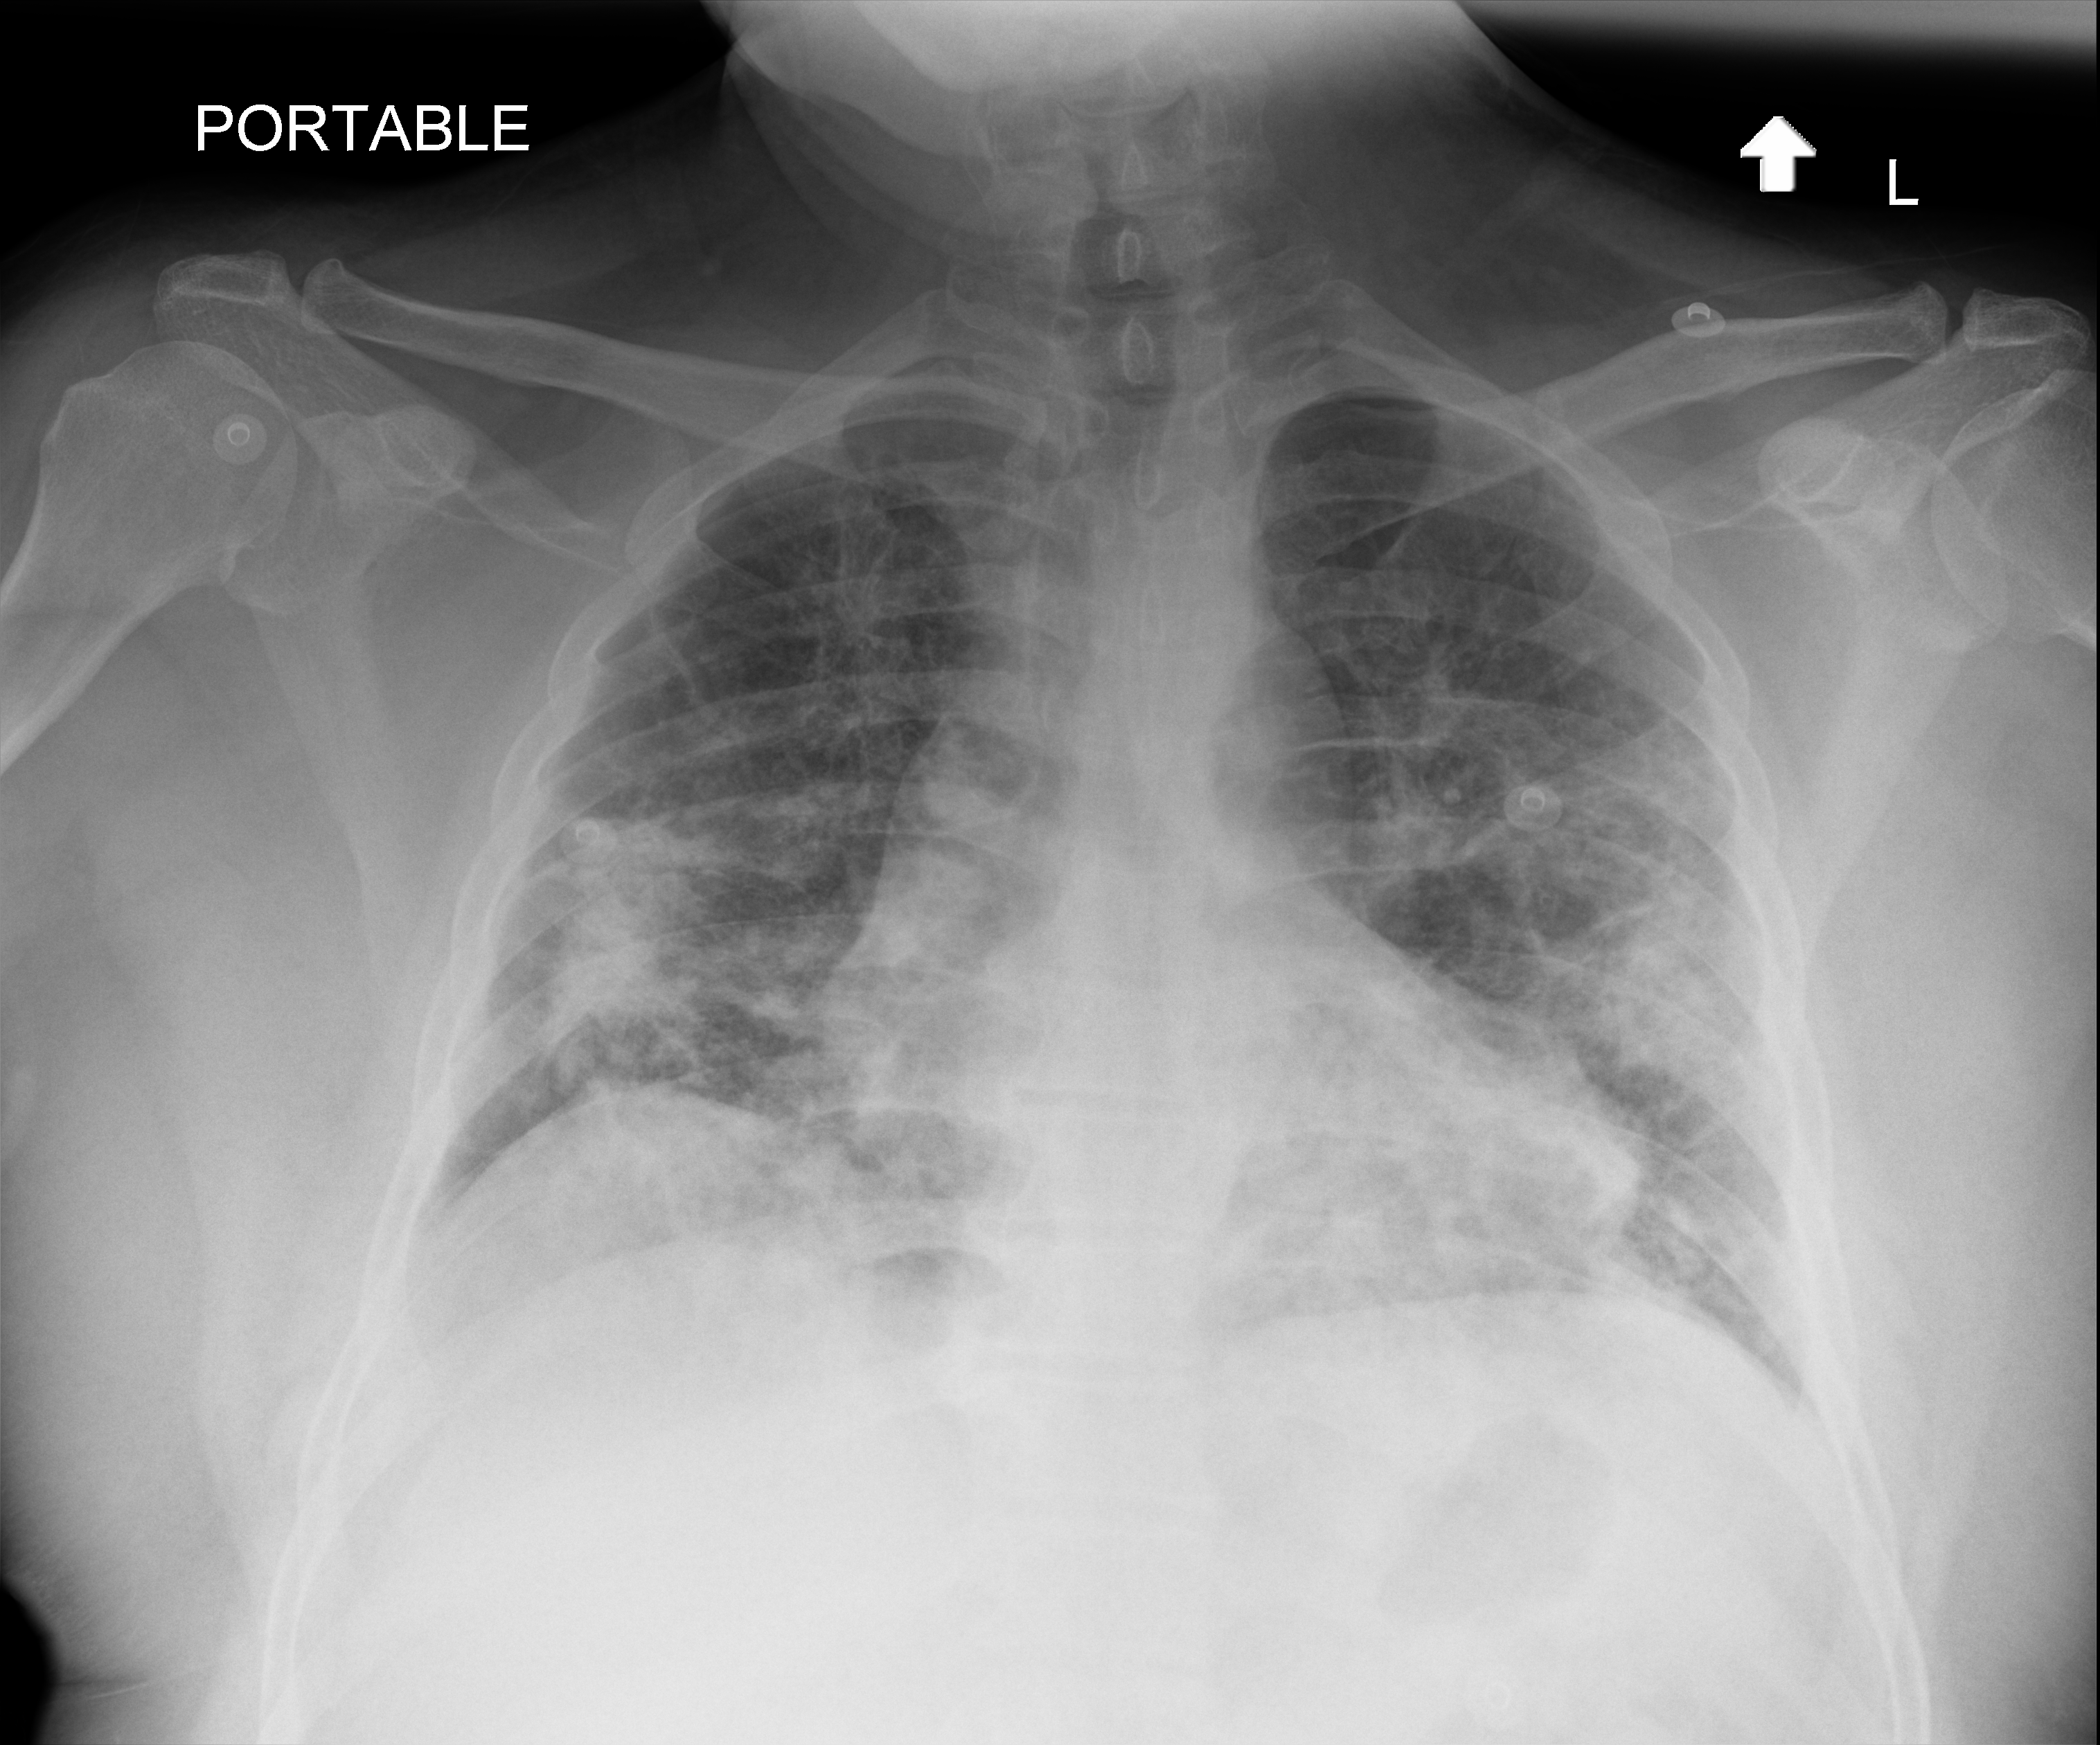
Chest radiograph (digital radiography), anteroposterior (AP) projection. Male patient hospitalised with COVID-19, age 18–59 years.
Hospital-stay facts (about this admission, not read from this image; timing relative to this image not recorded):
- admitted to intensive care during this hospital stay: no
- mechanically ventilated during this hospital stay: no
- length of hospital stay: 5 days